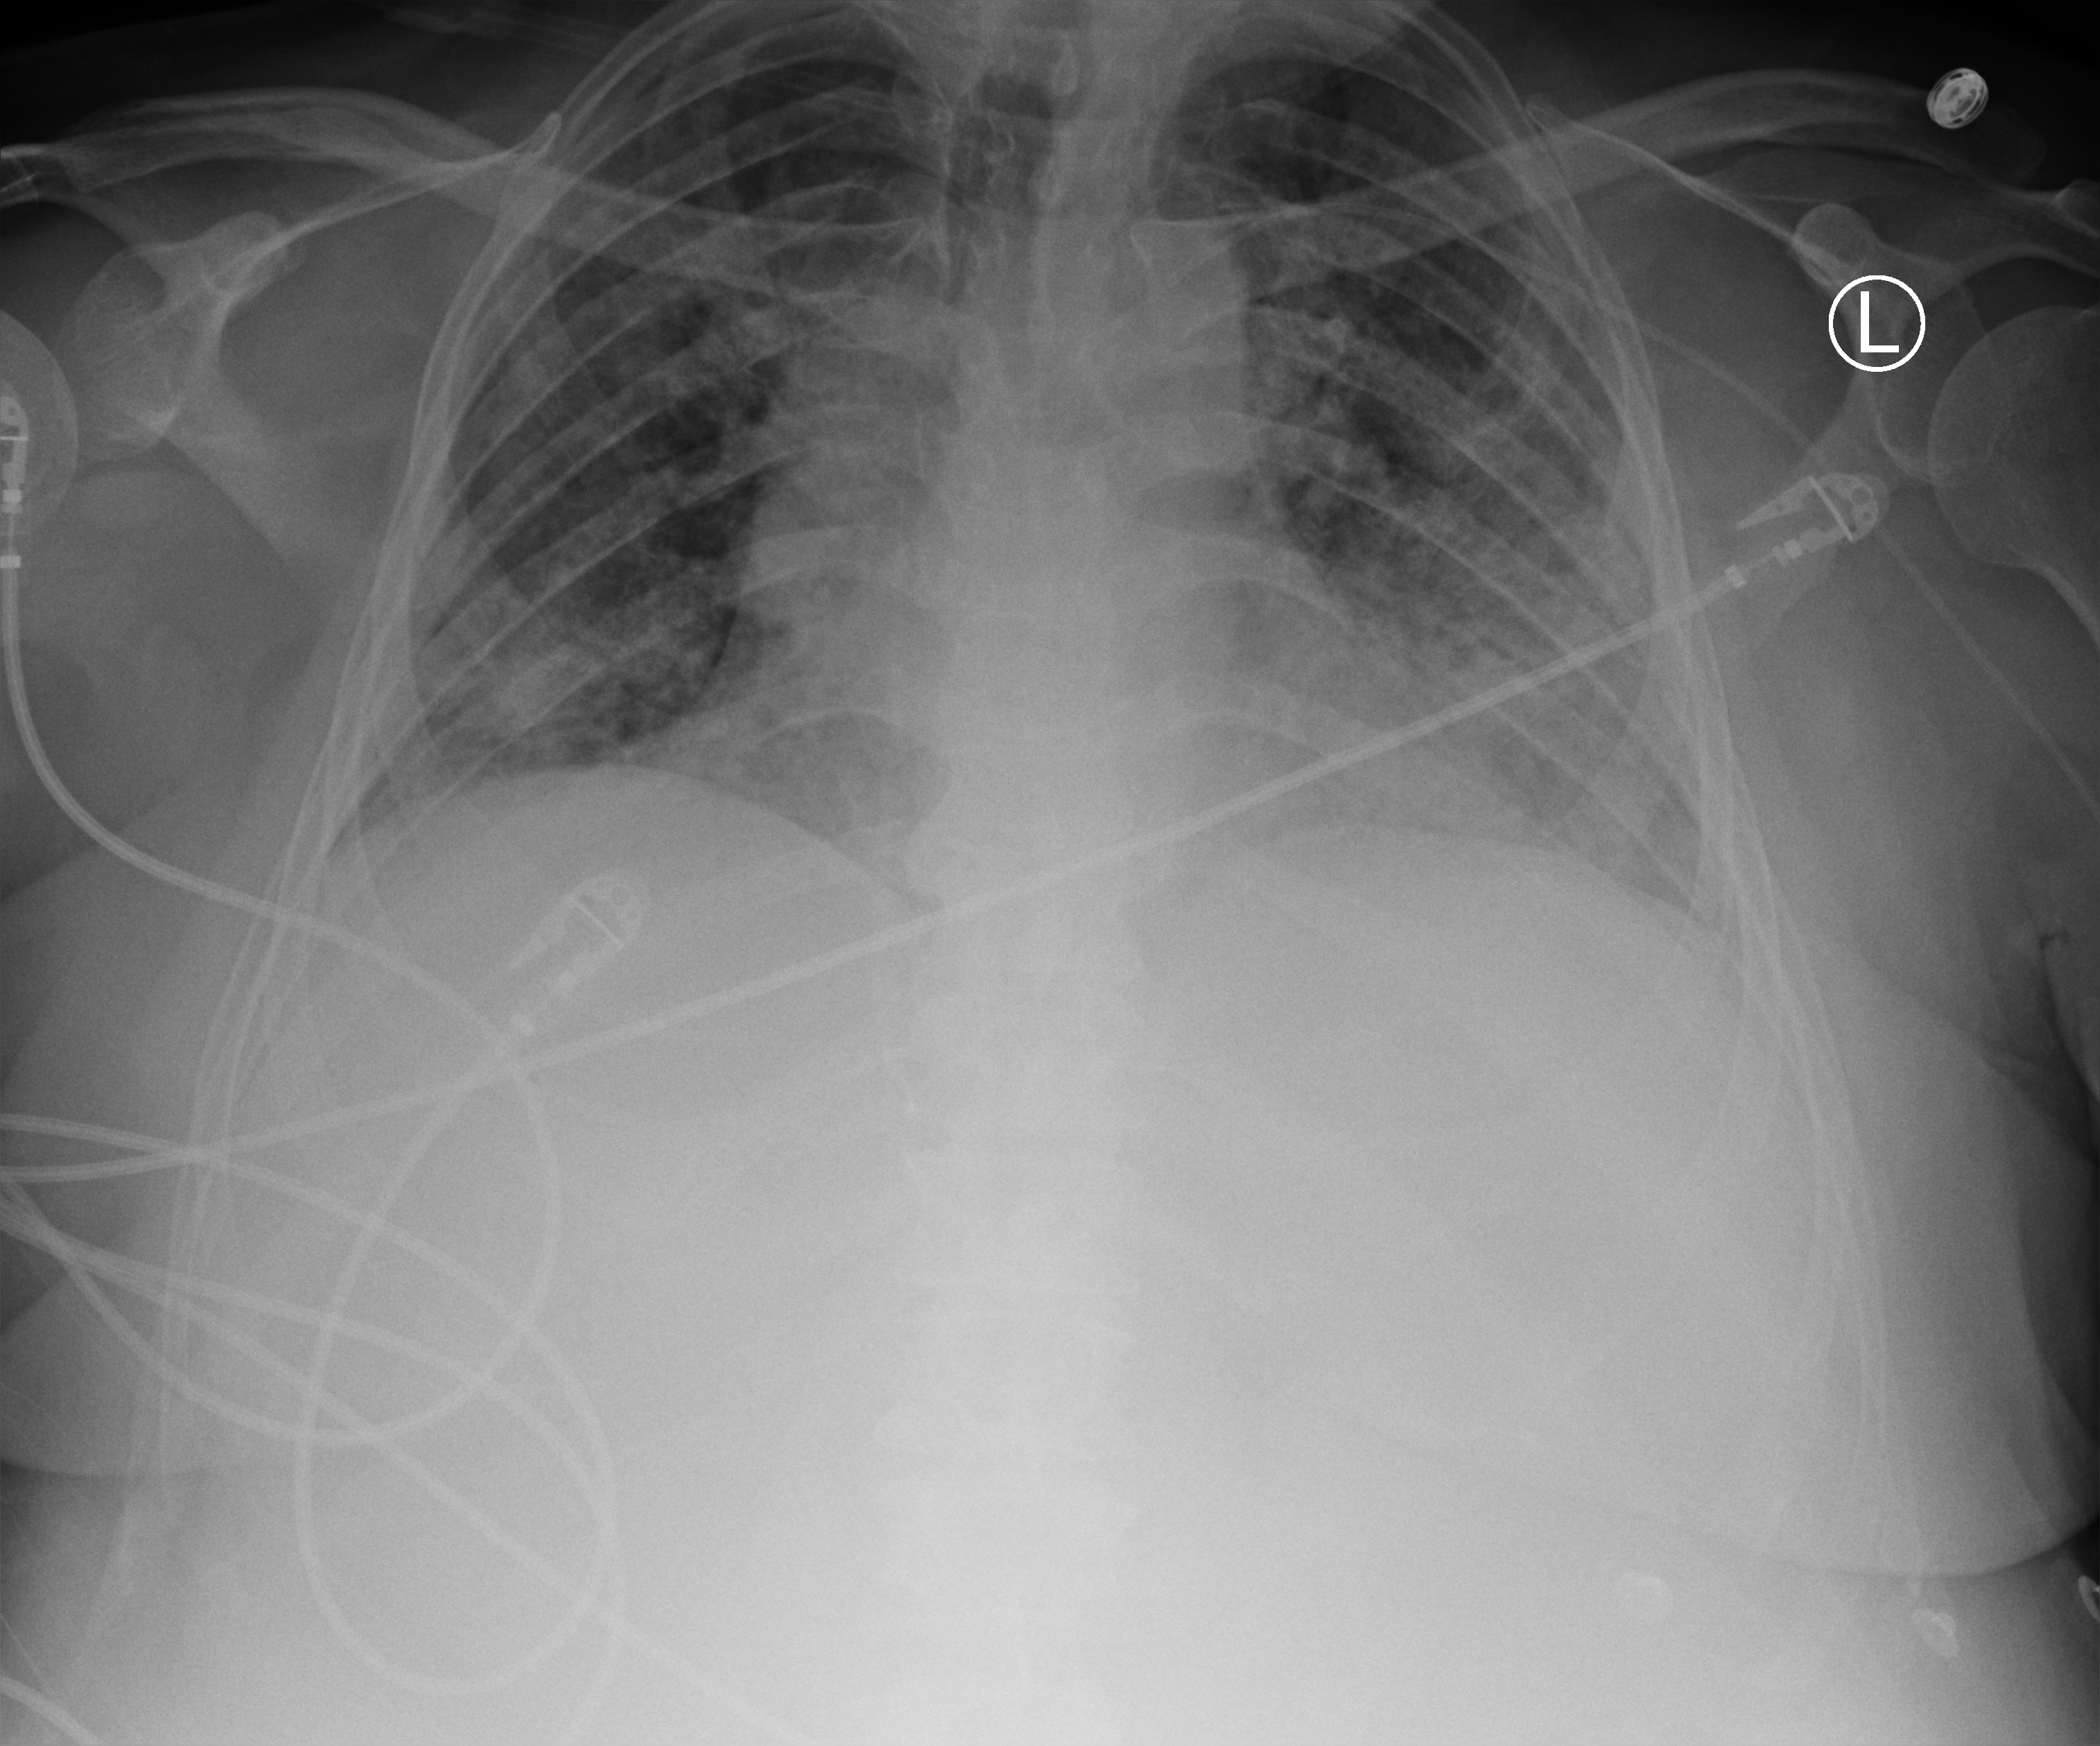
Chest X-ray (portable), anteroposterior (AP) projection. Male patient hospitalised with COVID-19, age 18–59 years.
Hospital-stay facts (about this admission, not read from this image; timing relative to this image not recorded):
- admitted to intensive care during this hospital stay: yes
- hypertension (admission record): yes
- diabetes (admission record): no